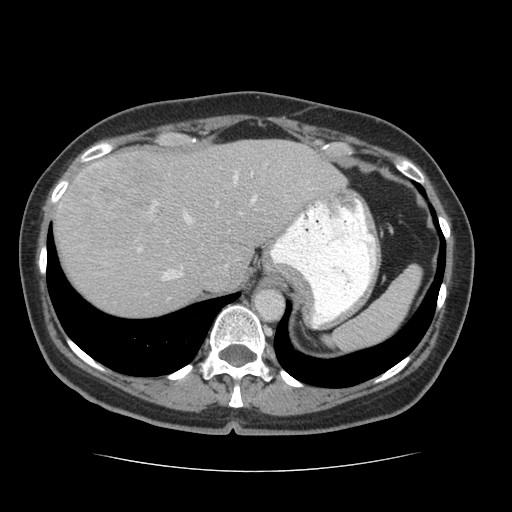
Contrast-enhanced abdominal CT (liver protocol), one axial slice. Position 52 of 75 along the scan axis. Reconstruction kernel STANDARD. 140 kVp. Soft-tissue window (W 400 / L 40 HU). 2.5 mm slice thickness. 512 × 512 image matrix, field of view 360 × 360 mm. Case-level facts recorded for this patient, not image findings: diagnosis: hepatocellular carcinoma (patient treated with transarterial chemoembolisation; whether this scan precedes or follows treatment is not stated here); TNM stage (as recorded): Stage-I; Child-Pugh class: A; tumour differentiation: moderately differentiated.
Outlined on this slice (semi-automatically segmented with operator editing):
- abdominal aorta: bounding box [x1, y1, x2, y2] px = [254, 289, 284, 319]
- liver parenchyma outside the tumour (the mass and vessels are separate outlines, so this box may not span the whole liver): [54, 140, 346, 316]
- mass: [66, 153, 173, 252]
- liver vessels: [60, 171, 258, 281]